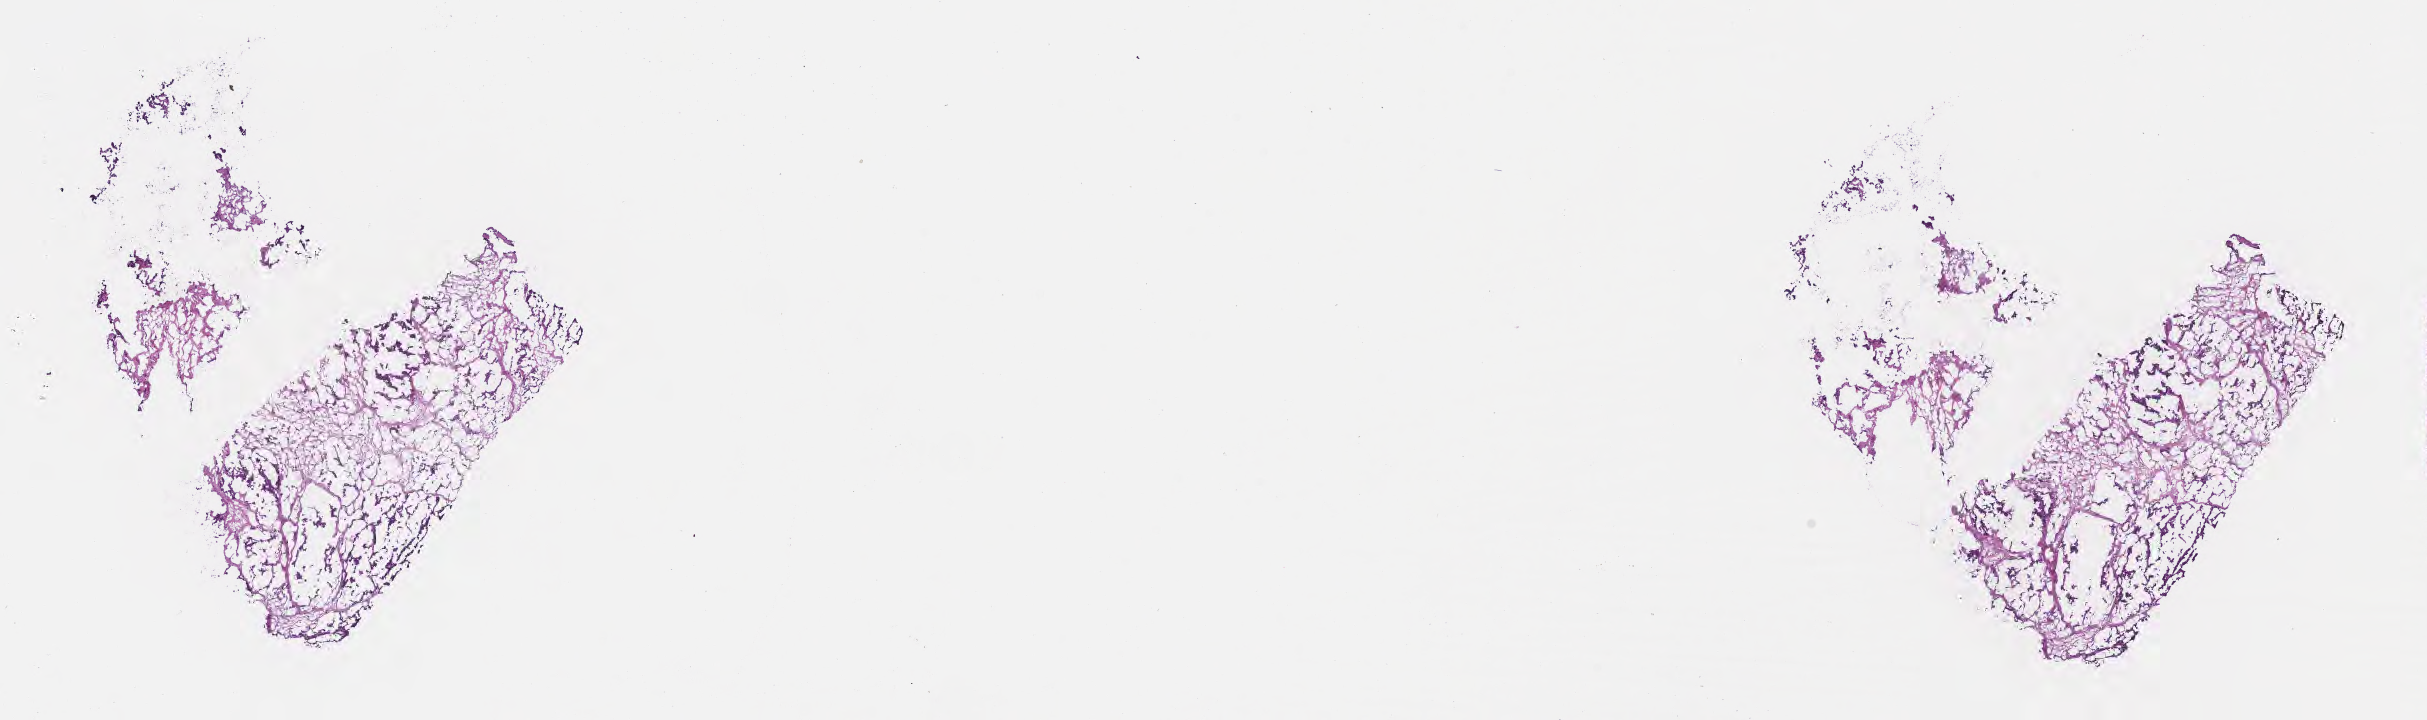
Haematoxylin and eosin whole-slide image, a low-resolution overview of the entire scanned area, about 19.6 x 5.8 mm; cryosection; specimen: metastatic tumor tissue, resected from pleura. Patient: male, age at initial diagnosis 12 years. Slide review estimates, as recorded: tumor cells 100%, tumor nuclei 40%, stromal cells 0%, necrosis 0%, normal cells 0%. Inflammatory infiltration, as recorded: lymphocyte infiltration 0%, monocyte infiltration 0%, neutrophil infiltration 0%.
Patient diagnosis (primary): Mixed type rhabdomyosarcoma. Section: bottom of the tissue portion.